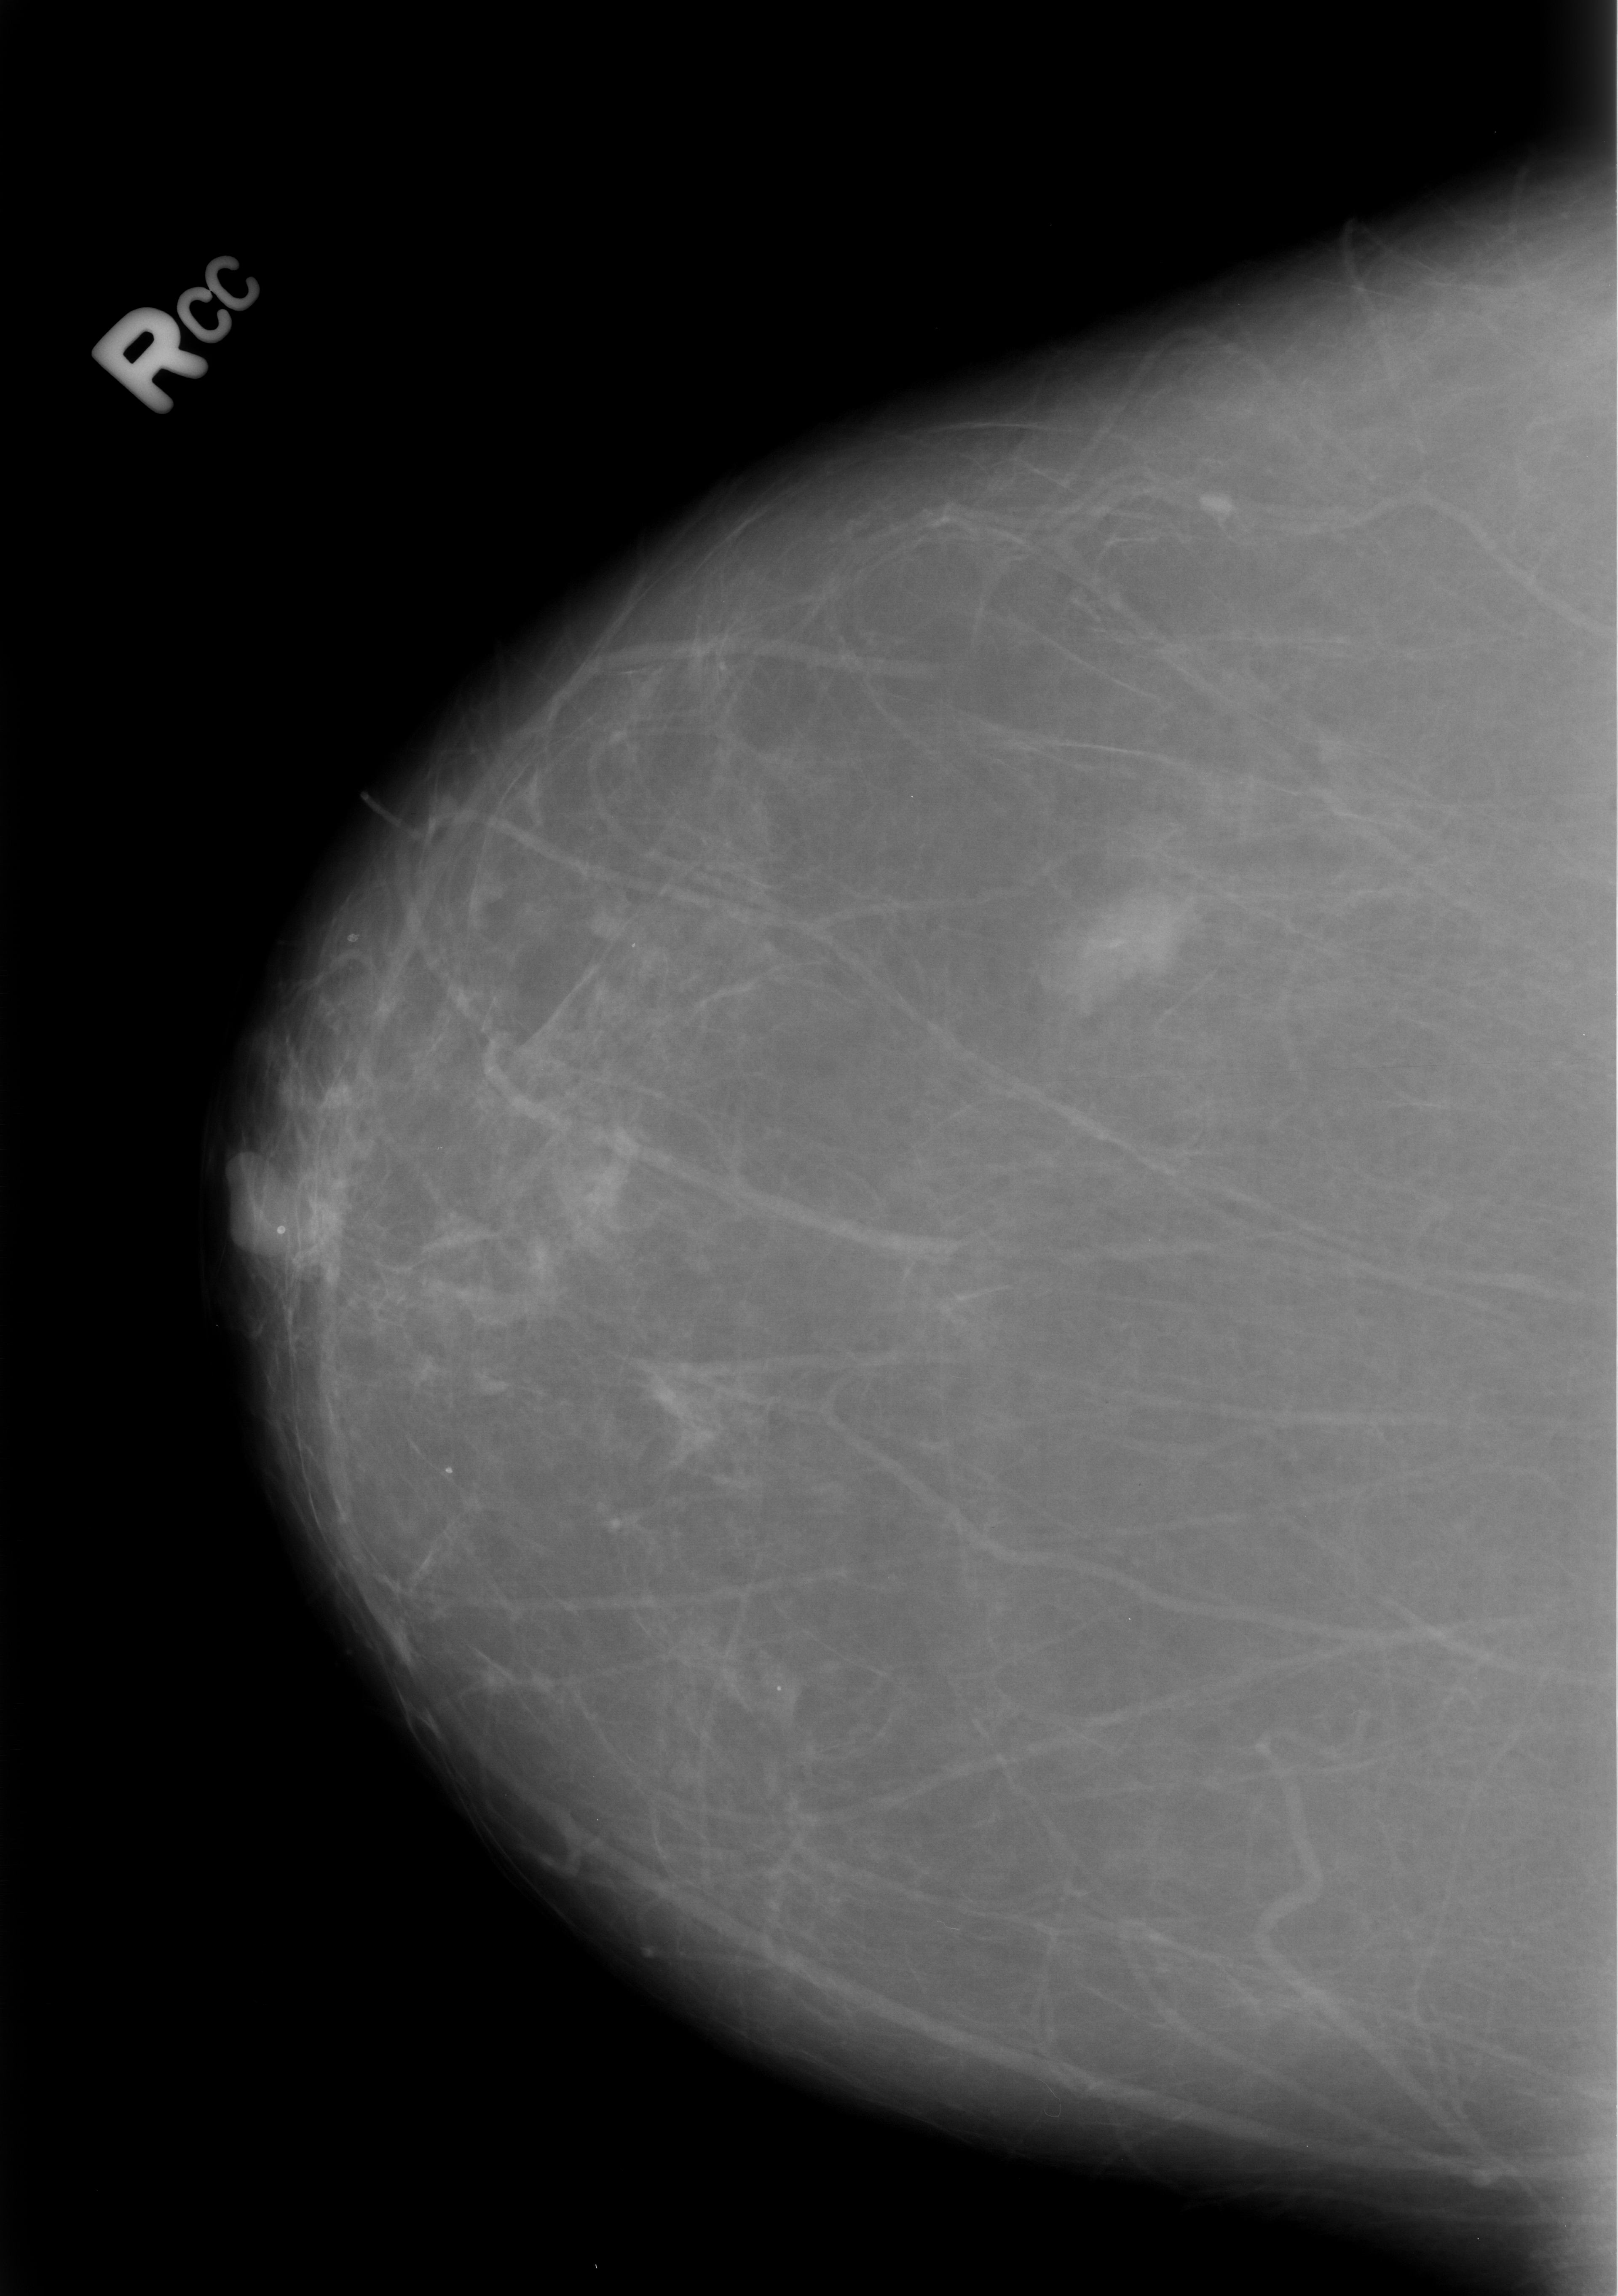
Scanned film-screen mammogram; right breast; CC view; BI-RADS breast density category 1 (scale 1–4); 1618 × 2296 image matrix.
Expert-marked regions of interest on this film, with their recorded descriptors:
- mass, shape lobulated / irregular, margins ill defined; BI-RADS assessment category 4; pathology (as recorded): benign: box from (x=1050, y=891) to (x=1183, y=1001) px